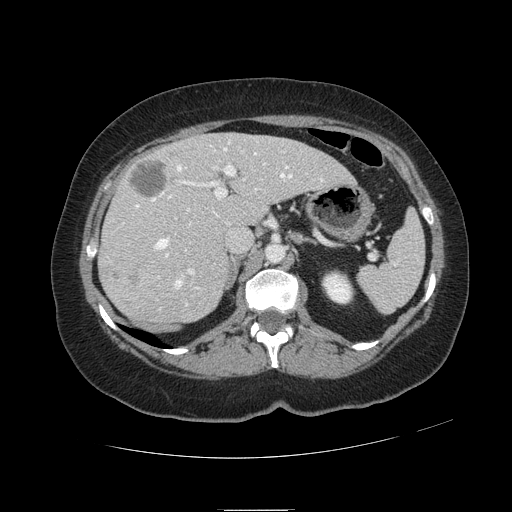
Contrast-enhanced abdominal CT, one axial slice; position 67 of 121 along the scan axis; 120 kVp; soft-tissue window (W 400 / L 40 HU); 2.5 mm slice thickness; 512 × 512 image matrix, field of view 400 × 400 mm. Female patient, age 52 years. Case-level facts recorded for this patient, not image findings: diagnosis: colorectal cancer liver metastases, imaged before liver resection; multiple liver metastases: yes; largest metastasis: 6.3 cm; disease in both lobes: no.
Outlined on this slice (manually delineated by an expert):
- hepatic veins: bounding box (x1, y1, x2, y2) in pixels: (136, 142, 323, 306)
- liver: (100, 134, 352, 323)
- planned liver remnant (the part of the liver to remain after resection): (167, 134, 353, 225)
- portal vein (with intrahepatic branches): (122, 163, 265, 278)
- liver metastasis: (130, 160, 168, 197)
- liver metastasis: (128, 271, 139, 283)